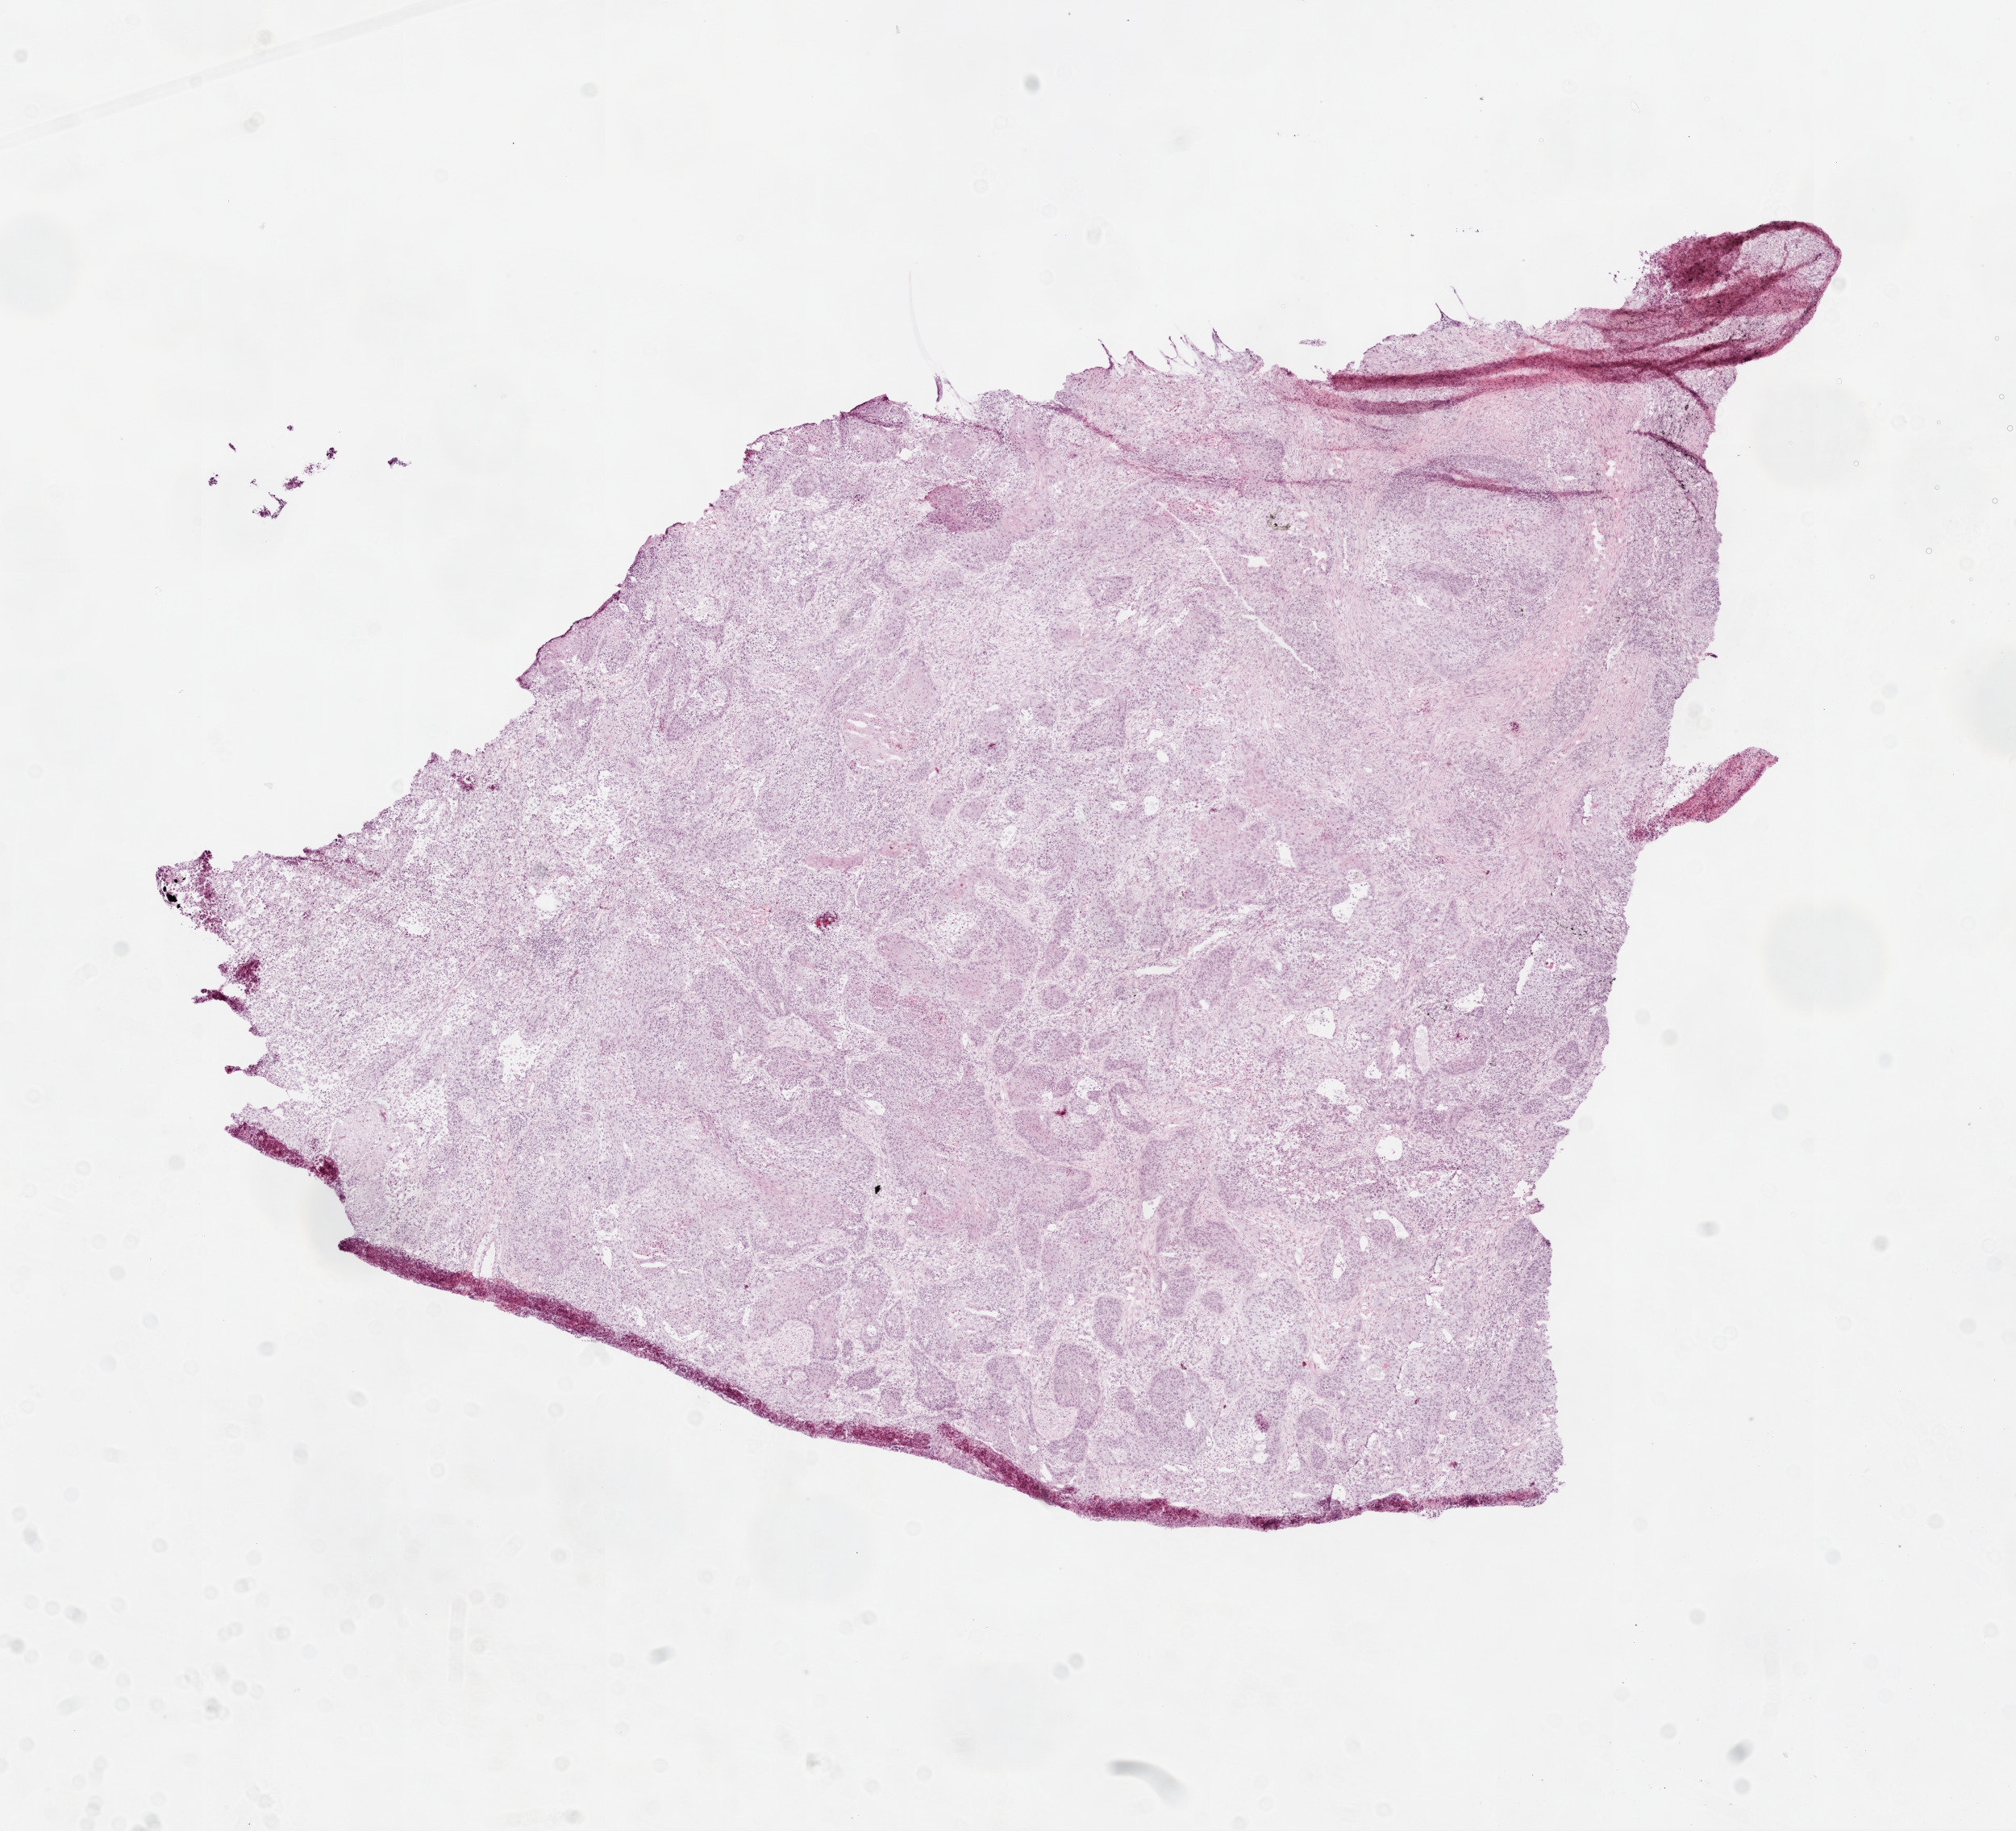
H&E-stained whole-slide image, shown as a low-resolution overview of the whole scanned area (about 10.0 x 9.1 mm, from a 20x scan); frozen section from the top of the tissue portion; sample: primary tumour, lung. Patient: male, age at initial diagnosis 70 years. Slide review estimates, as recorded: tumour cells 80%, tumour nuclei 70%, normal cells 0%, stromal cells 15%, necrosis 5%.
TNM: T2 N0 M0. AJCC pathologic stage: IB. Pathologic diagnosis: Squamous cell carcinoma, NOS (upper lobe, lung).